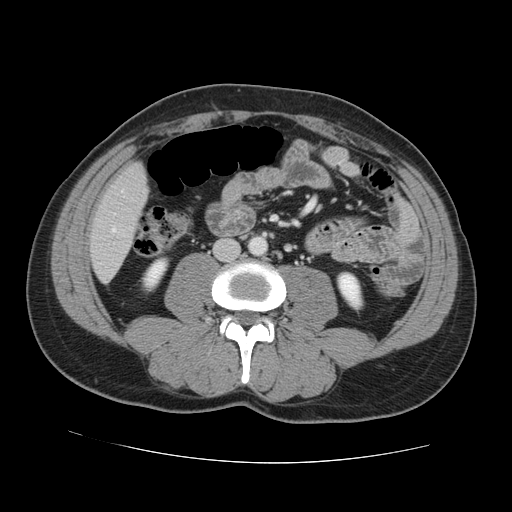
Contrast-enhanced abdominal CT, one axial slice. Slice 24 of 131 in the series (ordered by position). 120 kVp. Intravenous contrast given. Soft-tissue window (W 400 / L 40 HU). 512 × 512 image matrix, field of view 380 × 380 mm. Male patient, age 40 years. From the clinical record (not read from this slice): diagnosis: colorectal cancer liver metastases, imaged before liver resection; multiple liver metastases: yes; largest metastasis: 2.9 cm; chemotherapy before resection: yes.
Structures marked on this image (expert manual segmentation):
- hepatic veins: bounding box (x1, y1, x2, y2) in pixels: (112, 190, 123, 232)
- liver: (91, 165, 147, 281)